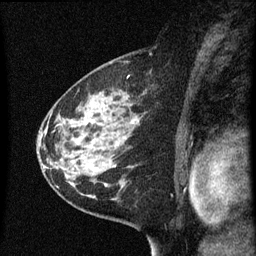
Breast MRI (dynamic contrast-enhanced), one sagittal slice. Slice 35 of 60 in the series (ordered by position). Dynamic contrast-enhanced series, image 2 of 3 at this slice position (ordered by acquisition). 1.5 T. TE 4.2 ms, TR 8 ms. 2 mm slice thickness. 256 × 256 image matrix, field of view 180 × 180 mm. Female patient, age 60 years.
Outlined on this slice (semi-automatically segmented with operator editing):
- analysis volume of interest (the breast-tissue region the enhancement analysis was run in; not a lesion): box from (x=48, y=82) to (x=147, y=183) px
- tumour enhancement mask (voxels above the 70 % enhancement threshold inside the analysis volume of interest): (x=86, y=116)–(x=137, y=171)